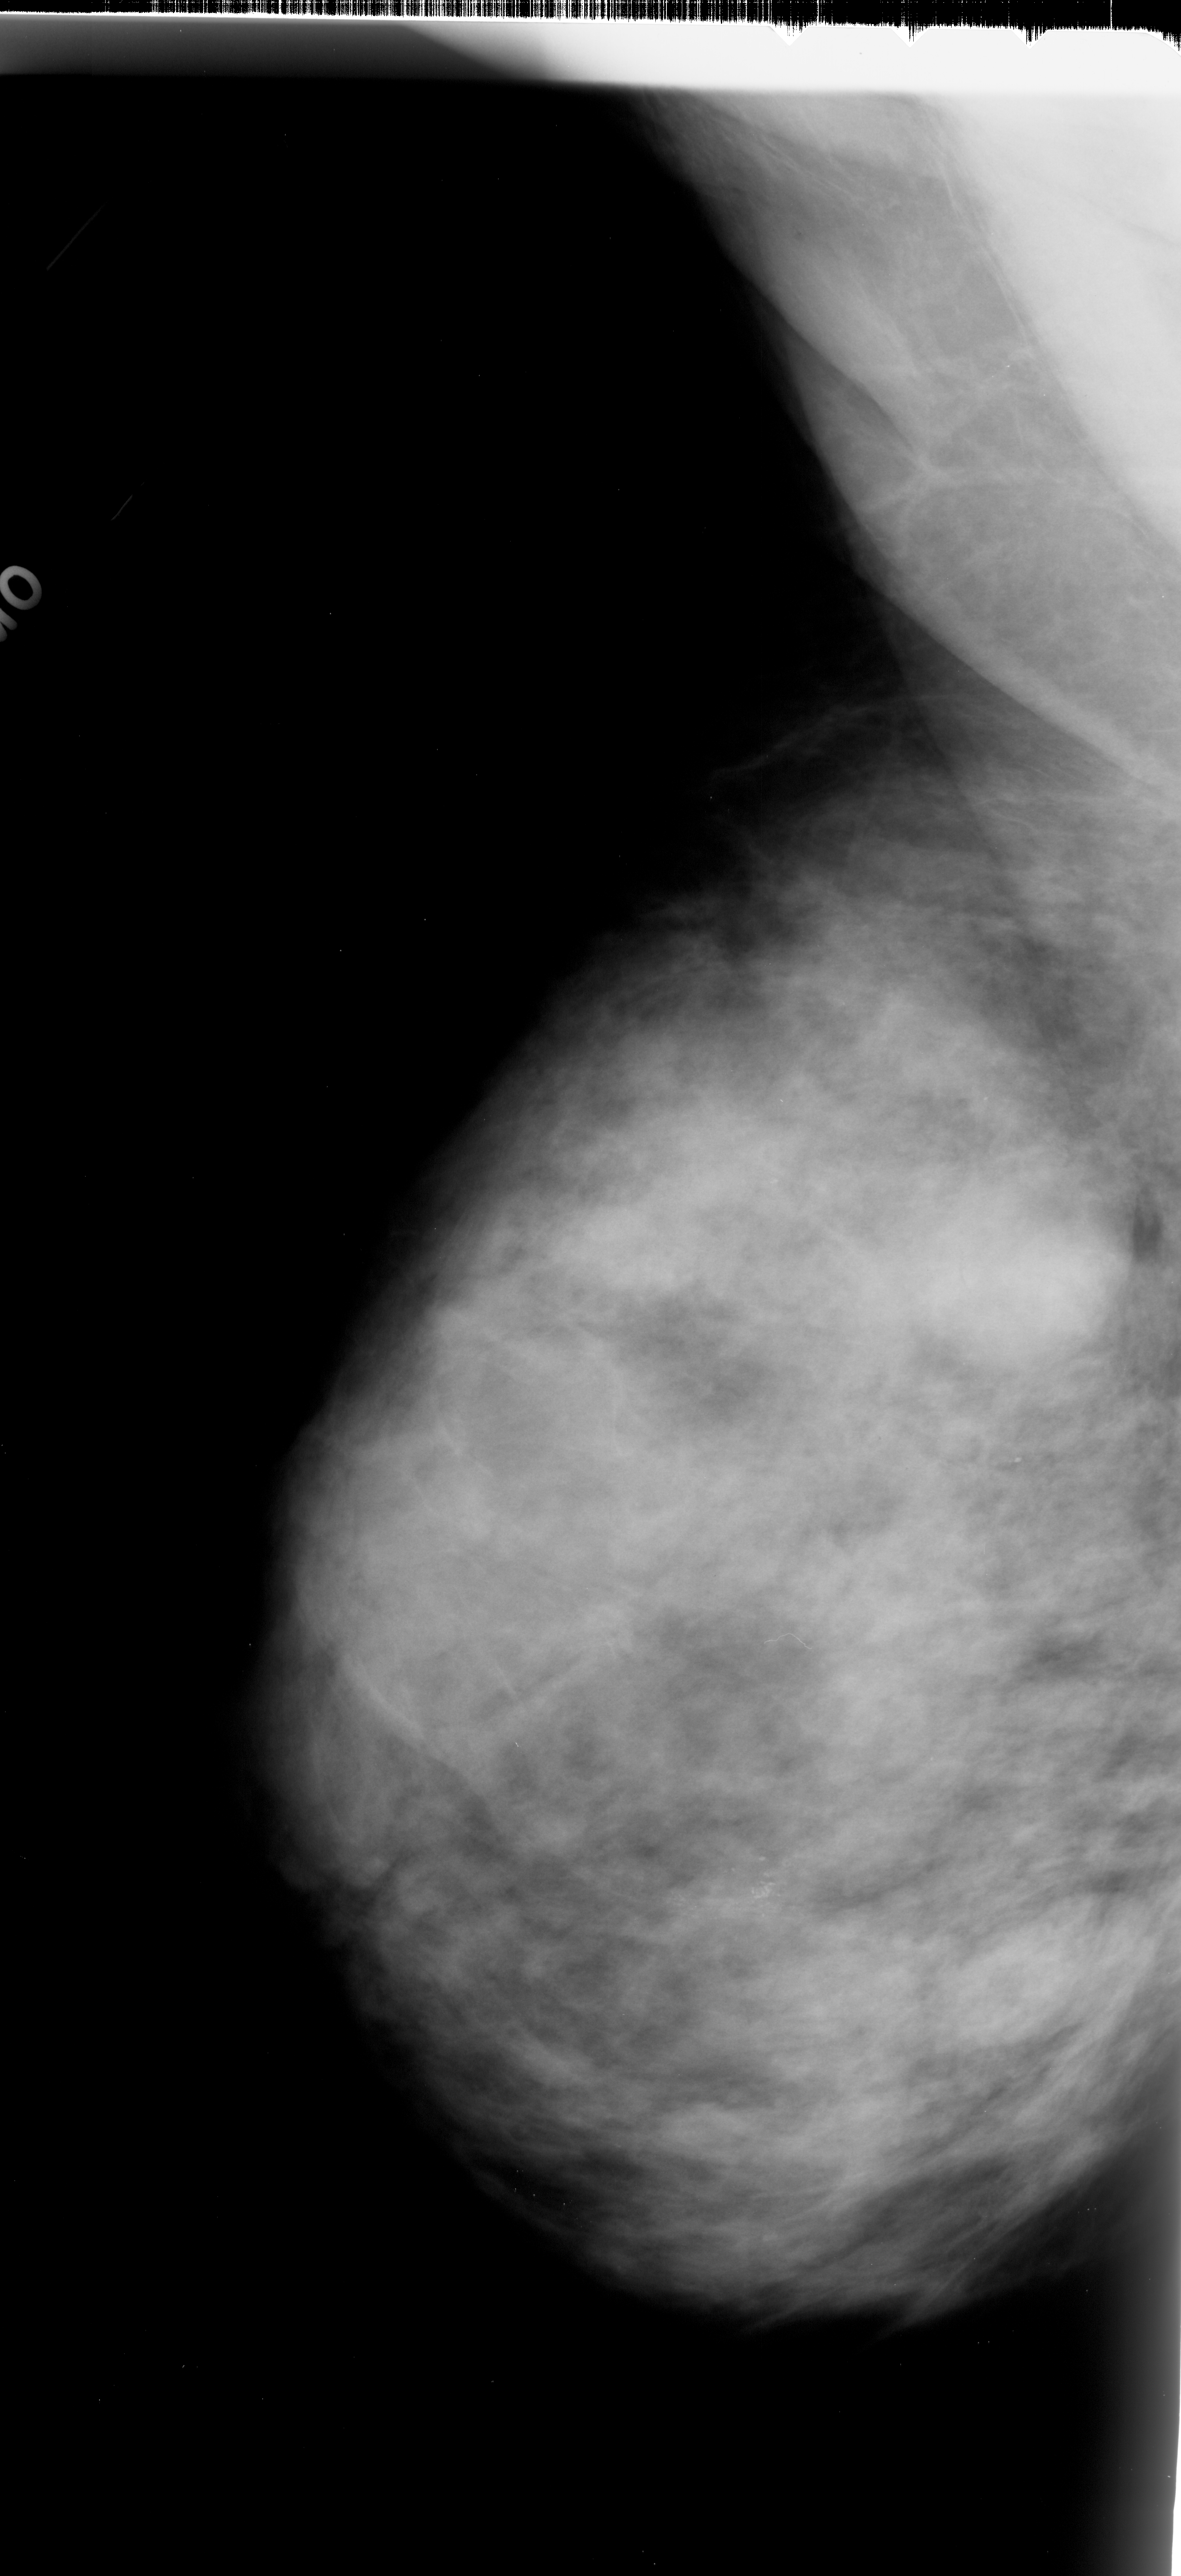
Scanned film-screen mammogram; left breast; MLO view; breast composition: extremely dense (BI-RADS density category 4 of 4).
- Abnormality record for this image: calcifications, morphology pleomorphic, distribution clustered; BI-RADS assessment category 4; subtlety rating 3 on a 1 (subtle) to 5 (obvious) scale; pathology (as recorded): malignant.